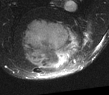
MRI of an extremity soft-tissue mass, one axial slice; T2-weighted fat-saturated; MR volume resampled by the dataset authors to the PET/CT grid (not the native acquisition matrix); 109 × 95 image matrix, field of view 106 × 93 mm. Male patient. From the clinical record (not read from this slice): histological type: synovial sarcoma; site of the primary tumour: left poplietal fossa.
Outlined on this slice (expert contour drawn on MRI and transferred to this co-registered scan by the dataset authors):
- gross tumour volume (mass): bounding box <22,19,75,68> (left, top, right, bottom; pixels)